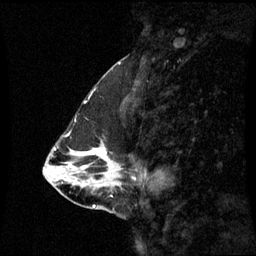
Breast MRI (dynamic contrast-enhanced), one sagittal slice. Position 26 of 60 along the scan axis. Dynamic contrast-enhanced series, image 2 of 3 at this slice position (ordered by acquisition). 1.5 T. TE 4.2 ms, TR 8.9 ms. 2.3 mm slice thickness. 256 × 256 image matrix, field of view 240 × 240 mm. Patient: female, 43 years. From the clinical record (not read from this slice): setting: breast cancer imaged before/during neoadjuvant chemotherapy; receptor status: HR-positive, HER2-negative.
Annotated regions visible in this slice (semi-automatically segmented with operator editing):
- analysis volume of interest (the breast-tissue region the enhancement analysis was run in; not a lesion): bounding box (x1, y1, x2, y2) in pixels: (78, 140, 123, 191)
- tumour enhancement mask (voxels above the 70 % enhancement threshold inside the analysis volume of interest): (90, 148, 98, 153)